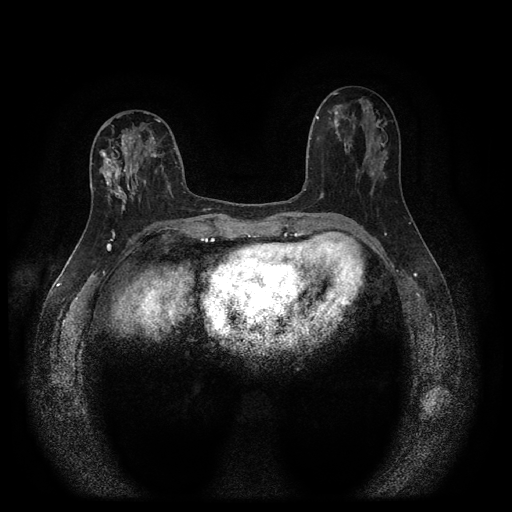
Breast MRI (dynamic contrast-enhanced, multi-phase), one axial slice. Position 42 of 116 along the scan axis. Dynamic contrast-enhanced series, time point 2 of 5 at this slice position (early post-contrast). 1.5 T. TE 2.7 ms, TR 5.4 ms. 512 × 512 image matrix, field of view 330 × 330 mm. Female patient, age 47 years.
Annotated regions visible in this slice (semi-automatic segmentation, software-assisted and operator-edited):
- breast lesion (labelled 'tumour' in the annotation; benign lesions carry a separate 'benign' label): bounding box [x1, y1, x2, y2] px = [99, 123, 158, 214]